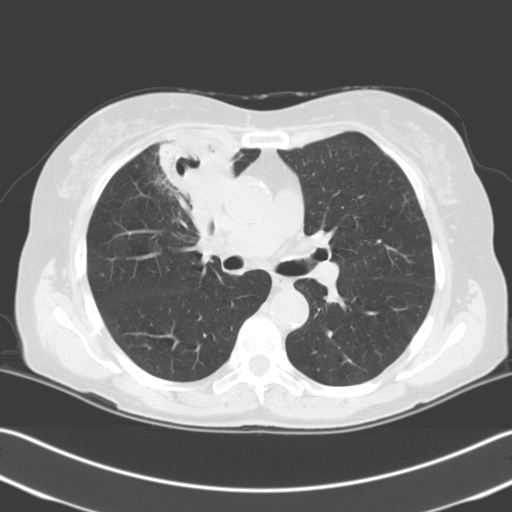
Low-dose screening chest CT, one axial slice. Slice 131 of 204 in the series (ordered by position). 140 kVp. Lung window (W 1500 / L -600 HU). 3.2 mm slice thickness. 512 × 512 image matrix.
Structures marked on this image (outlined manually by an expert reader):
- lesion 1 (tumor, upper lobe of right lung): bounding box [x1, y1, x2, y2] px = [159, 135, 239, 232]